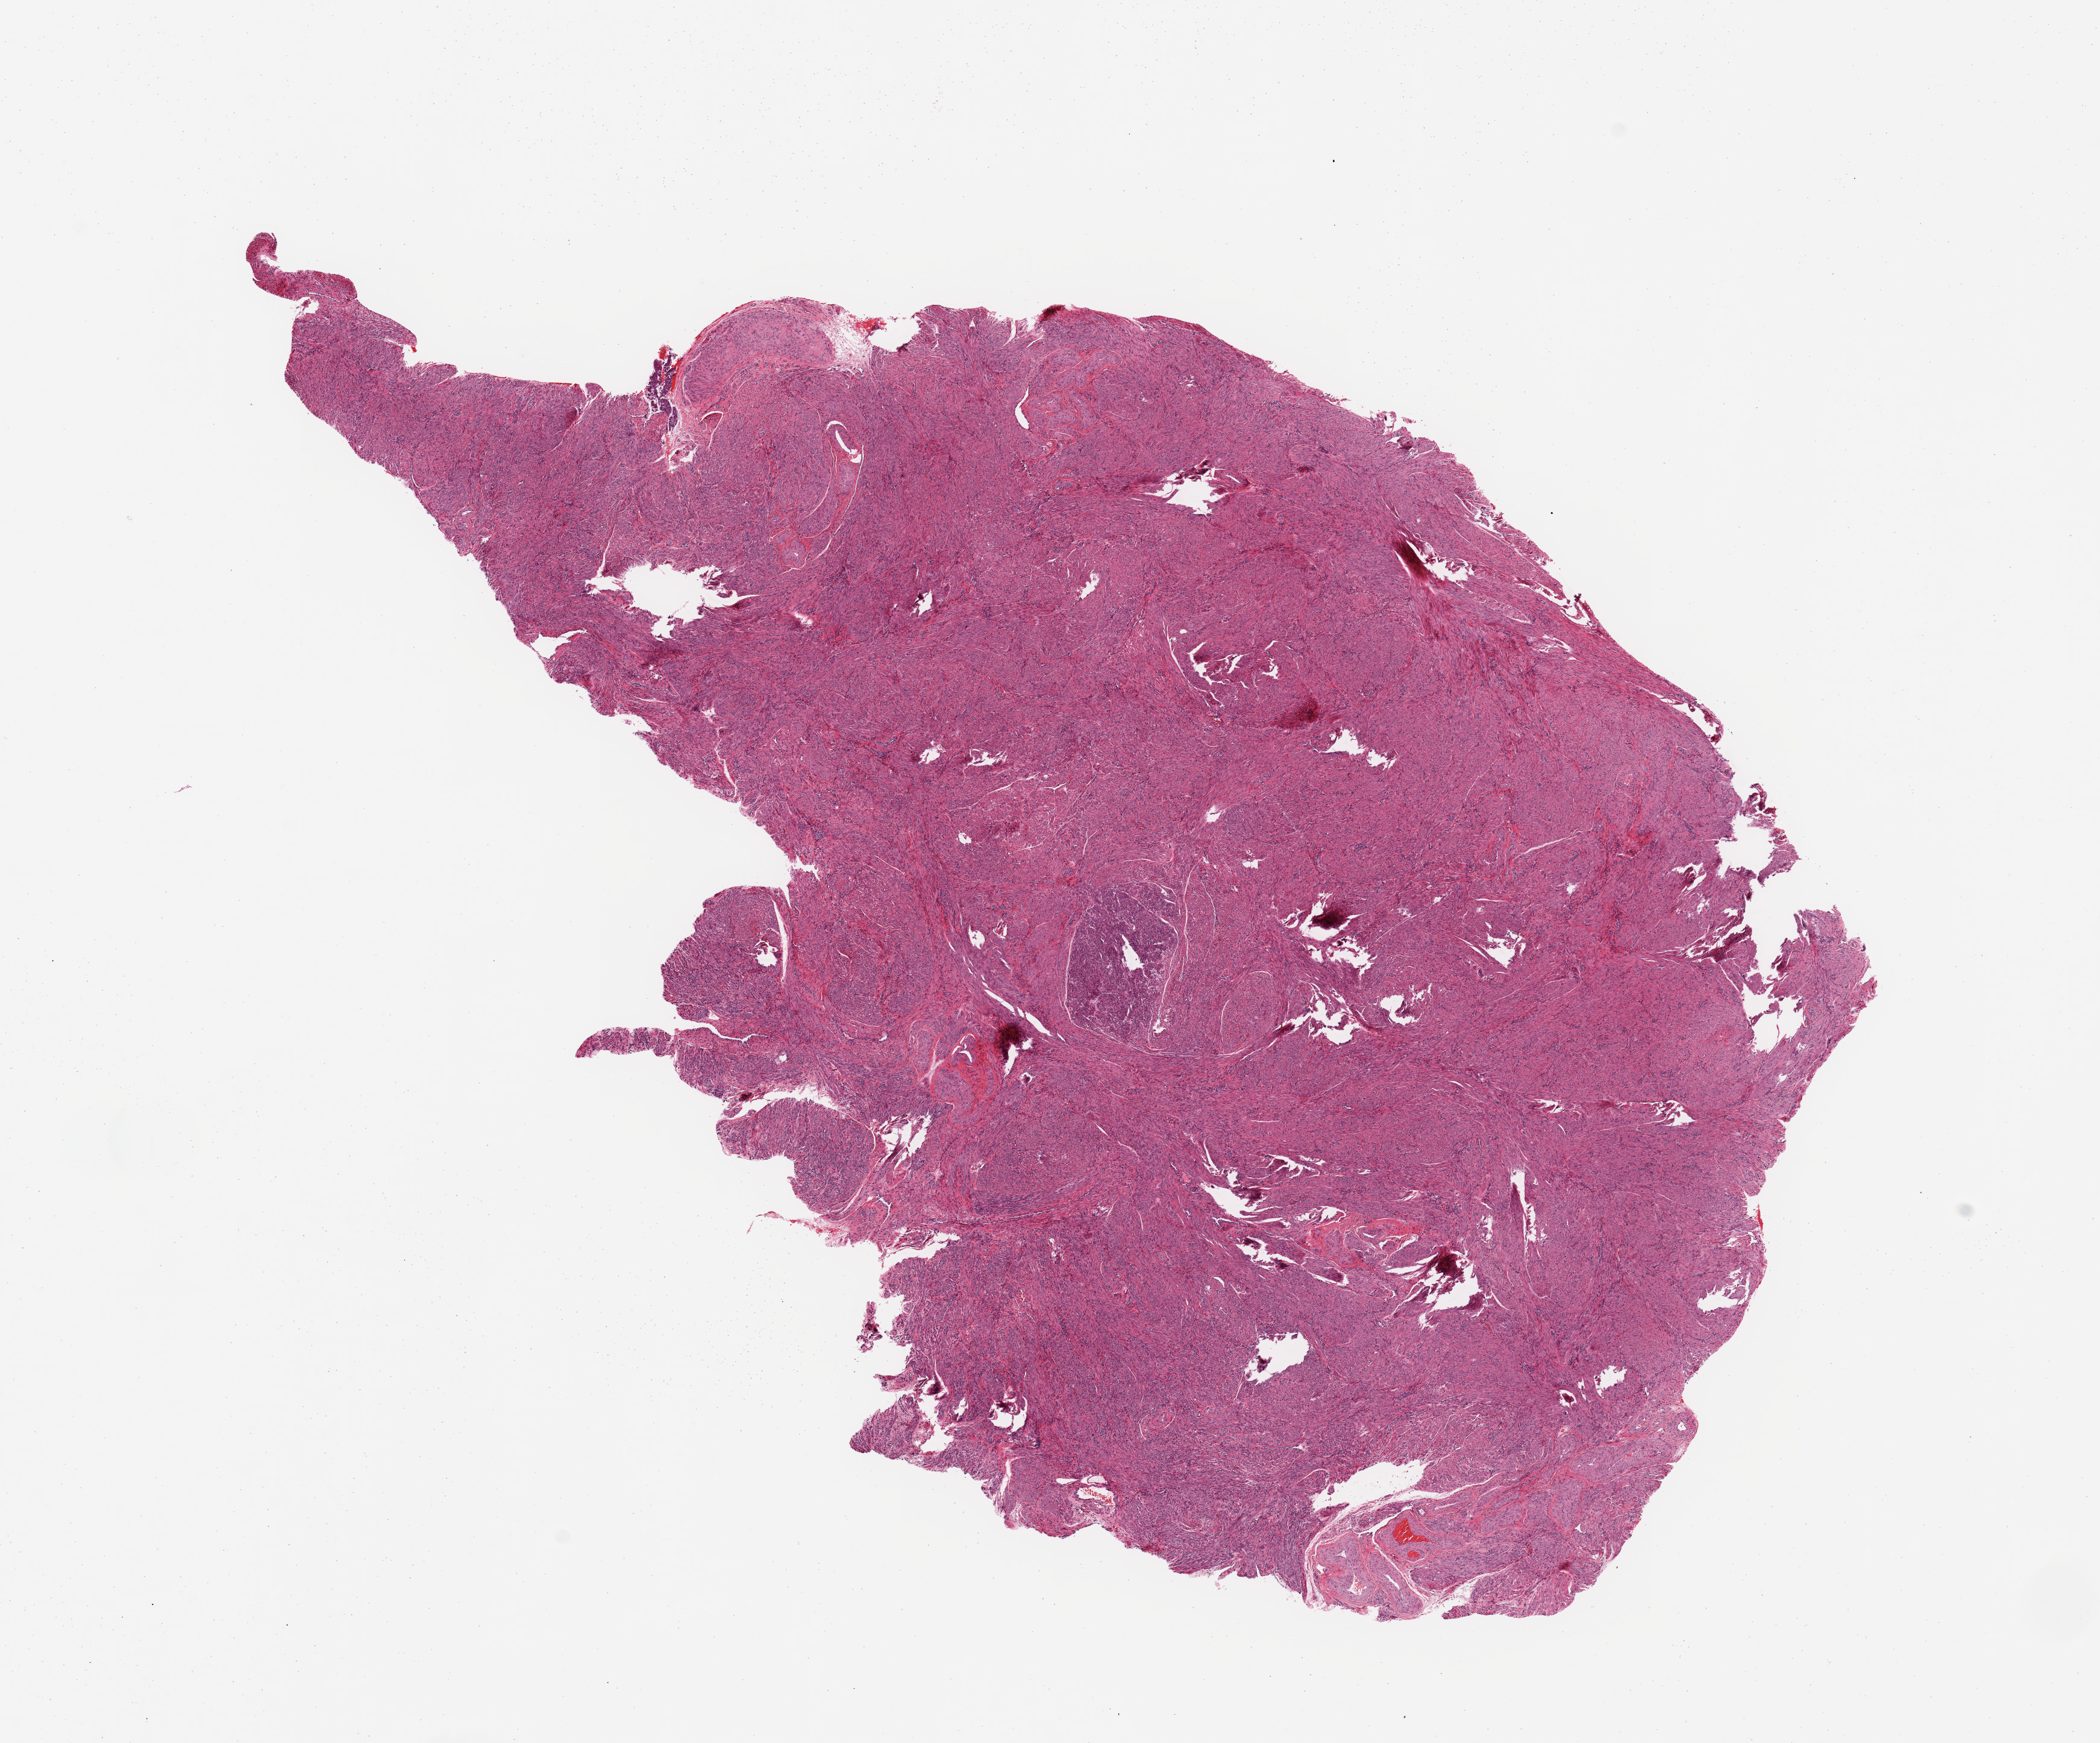
H&E whole-slide image, low-resolution overview of the scanned area, about 13.8 x 11.4 mm; normal (non-tumour) tissue sample, uterus. Patient: female, age 50 years.
* this section: normal (non-tumour) tissue from the same patient
* patient diagnosis: Endometrioid adenocarcinoma, NOS